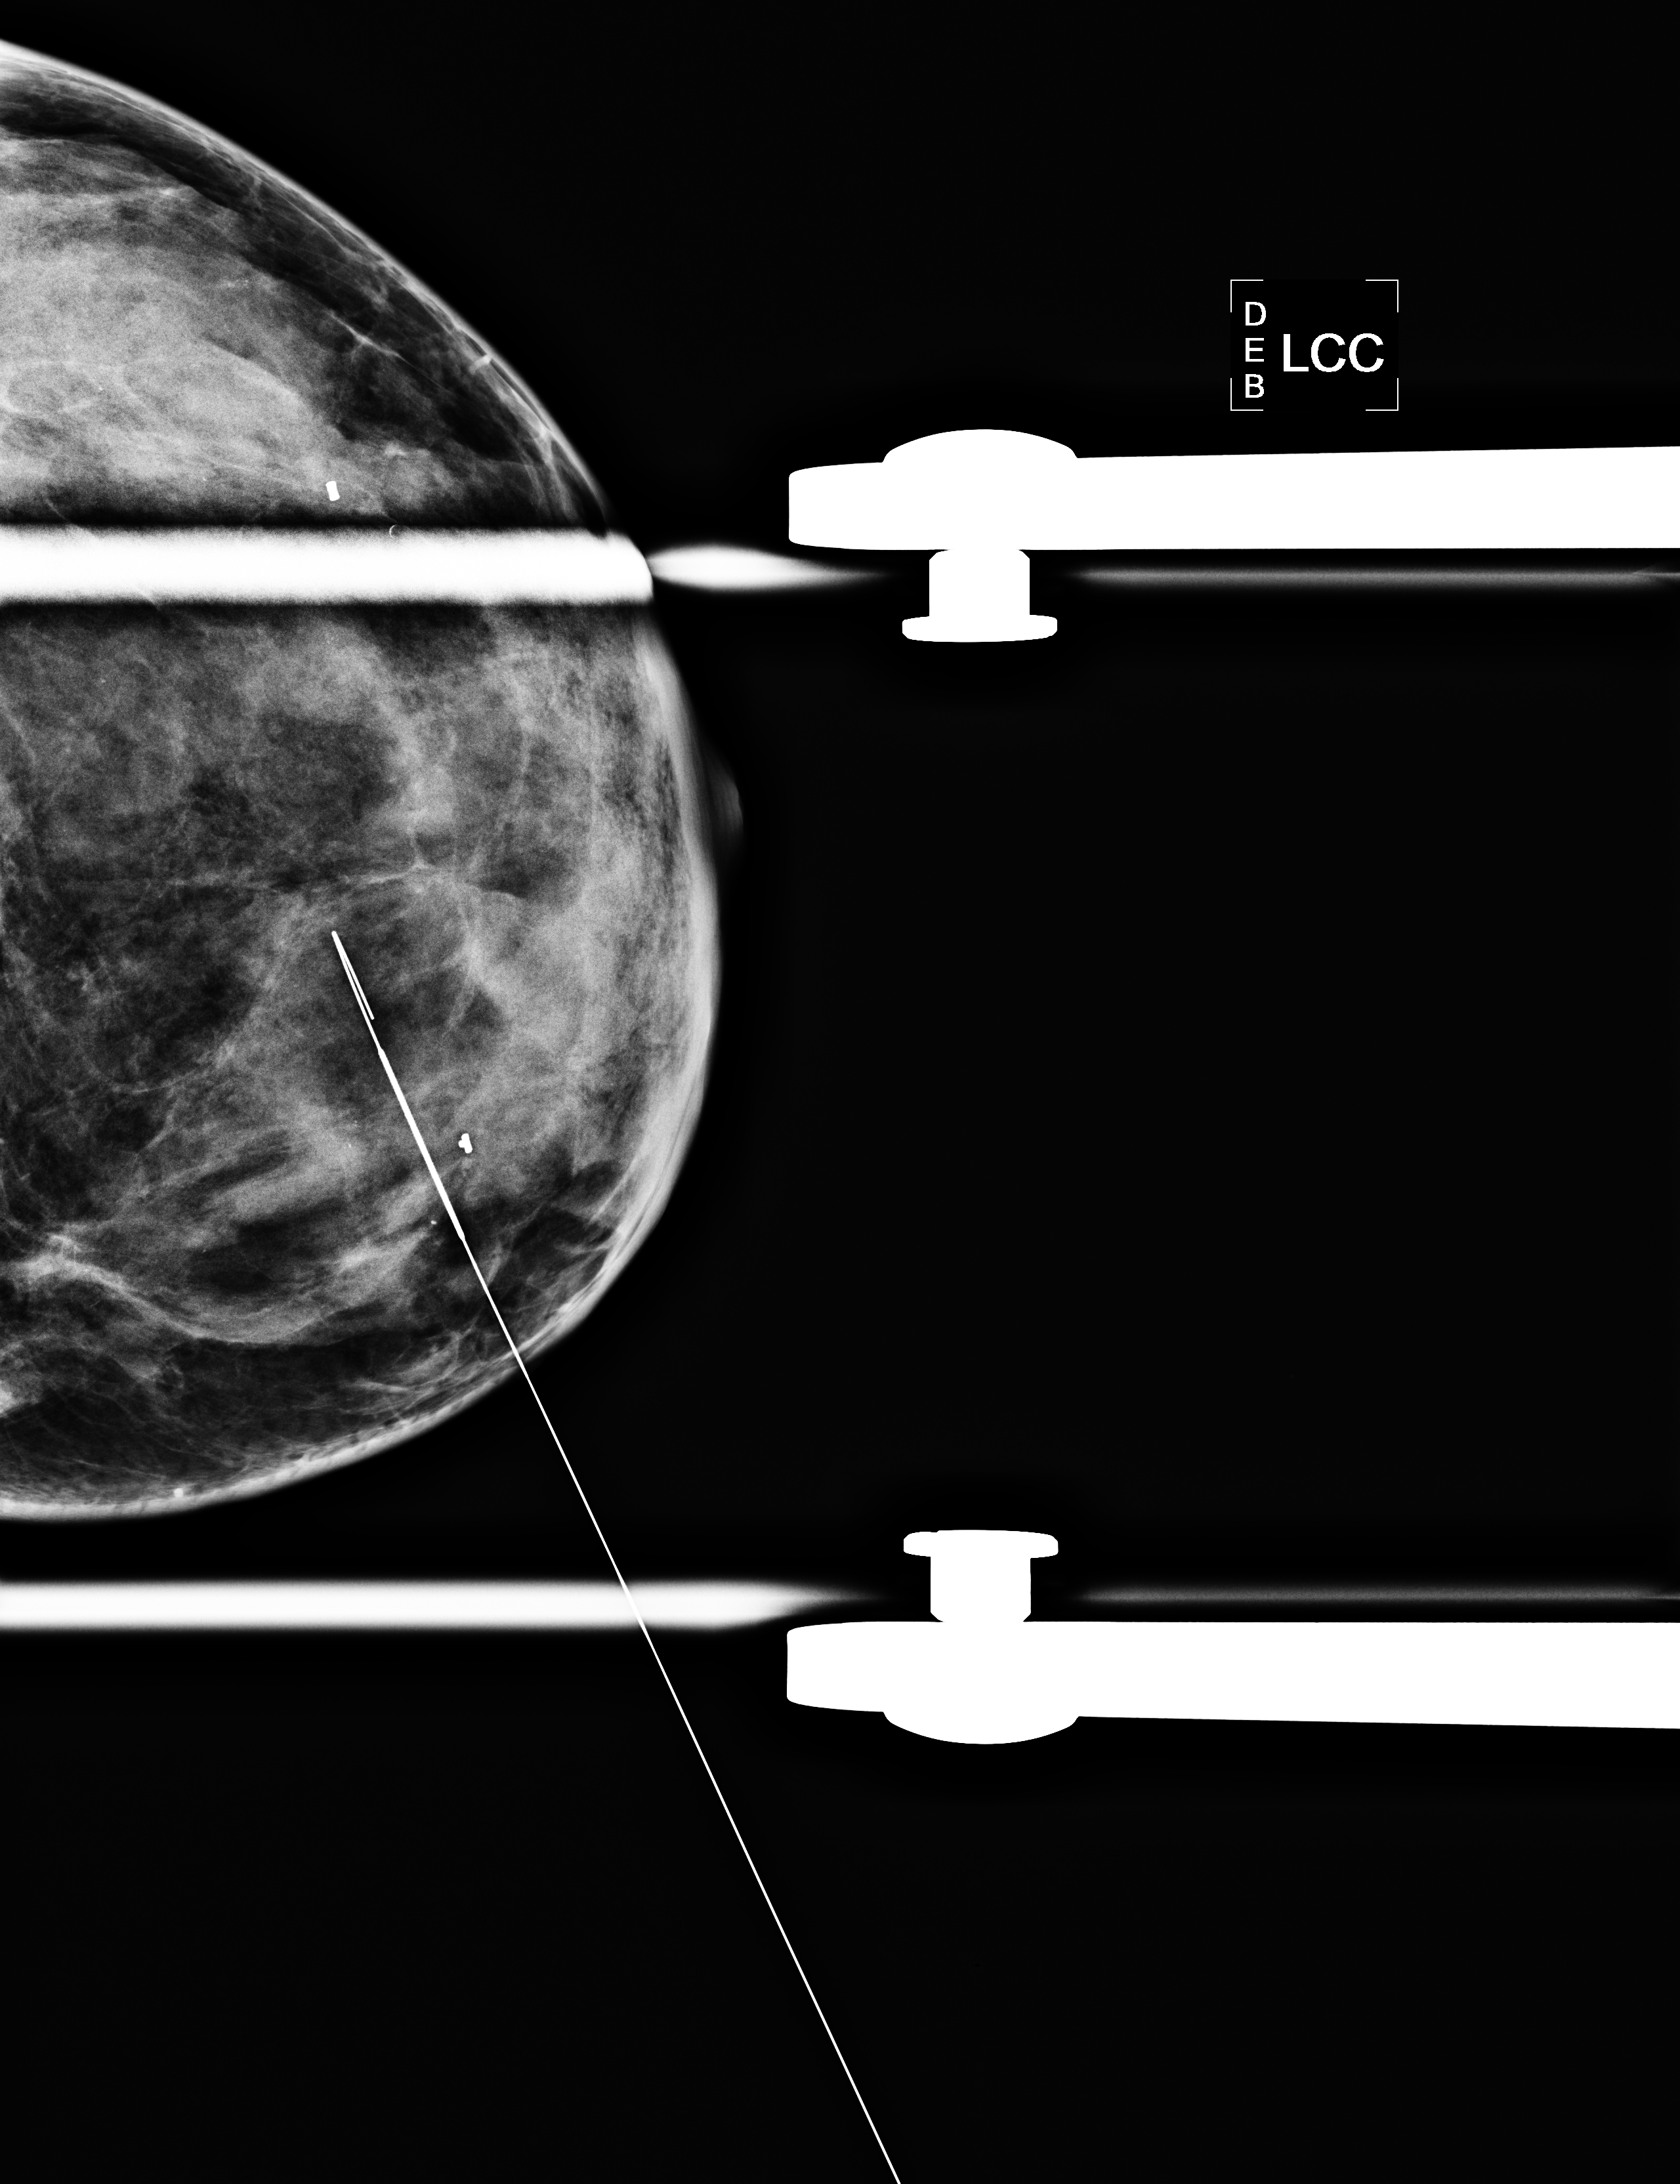
Needle-localisation mammographic view, left breast, CC view.
Pathology recorded for this patient (not read from this image): pathology diagnosis: ducta CA in situ (left breast); receptor status (as recorded): ER neg, PR neg, HER2 pos.